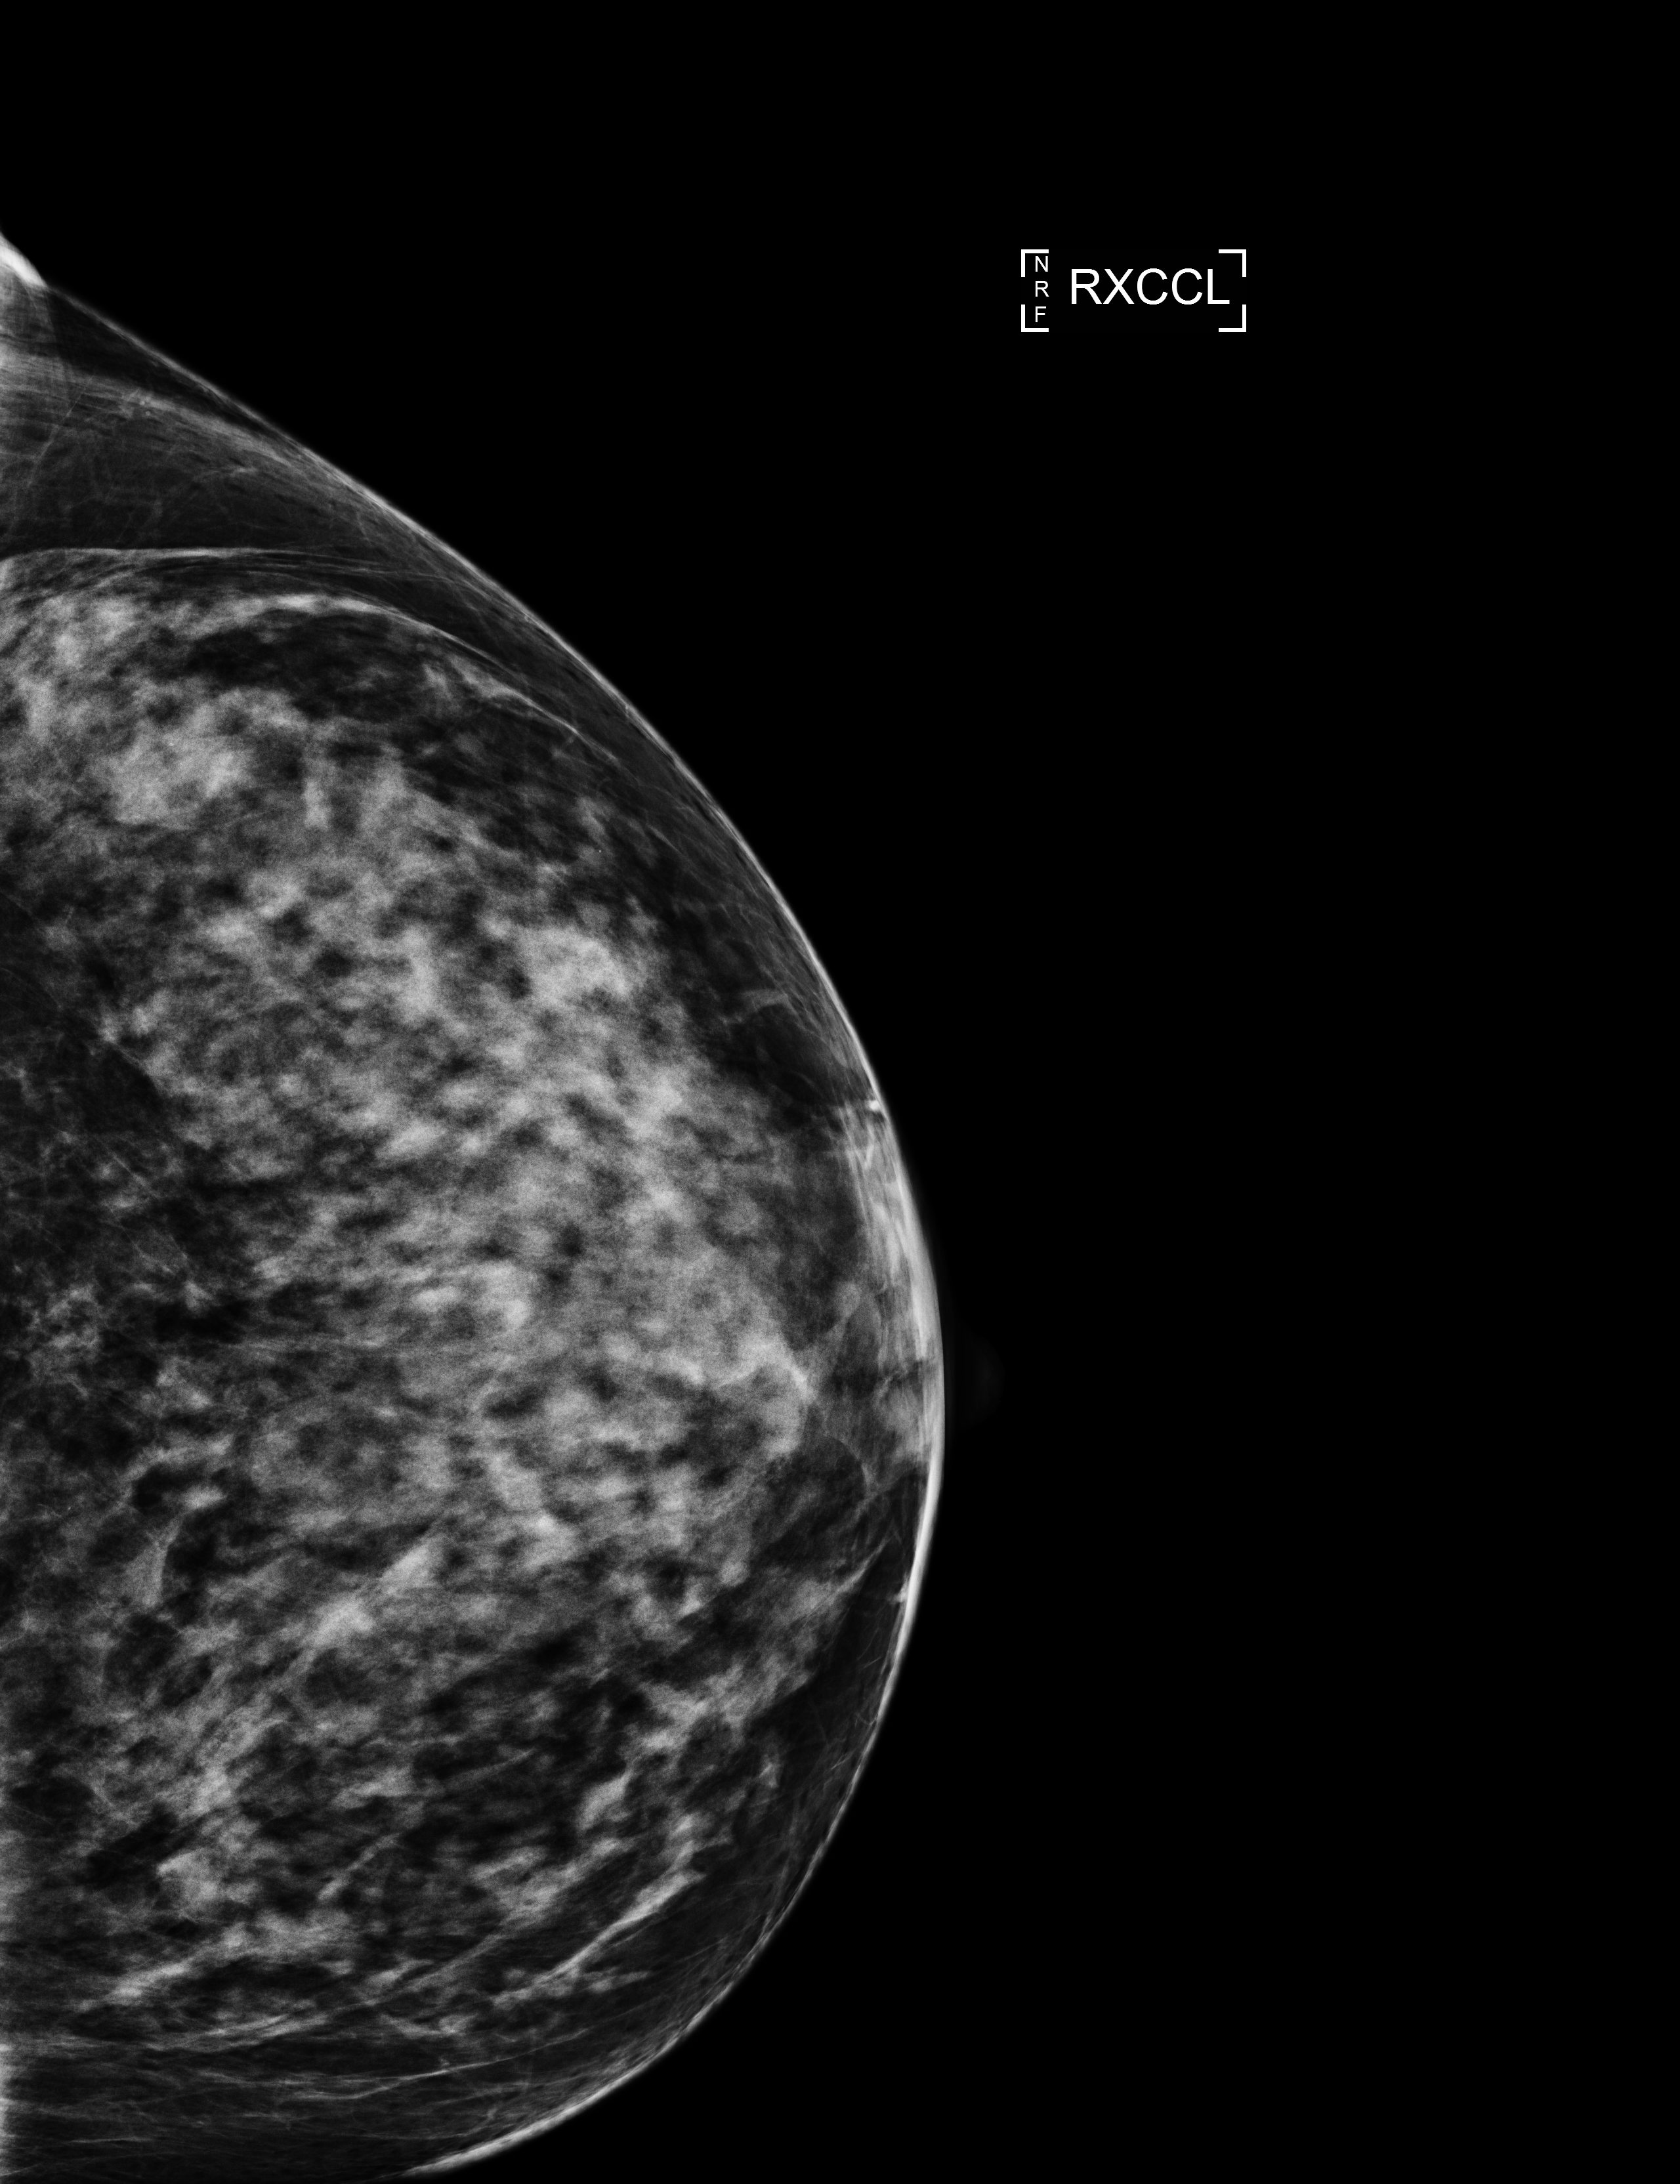
Full-field digital mammogram (FFDM); right breast; exaggerated CC view (lateral); screening examination; compressed breast thickness 68 mm; system: Selenia Dimensions. Female patient, age 60 years.
Breast density at the screening exam (both breasts): extremely dense (BI-RADS density category d). Final BI-RADS category for the screening round (tomosynthesis exam, both breasts): category 1. Recall: no recall after this screen.